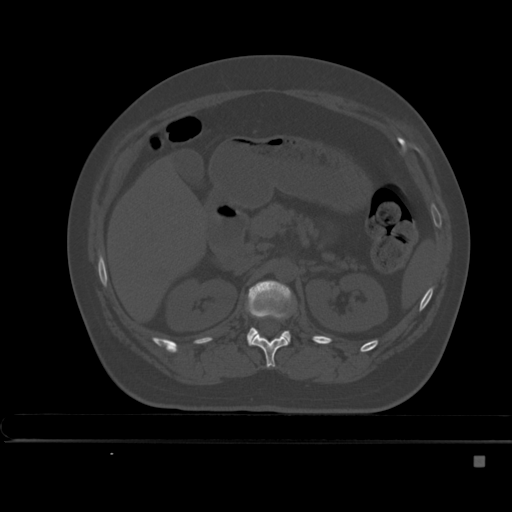
CT including the spine, one axial slice; position 205 of 495 along the scan axis; bone window (W 1800 / L 400 HU); 1.5 mm slice thickness; 512 × 512 image matrix, field of view 404 × 404 mm. Patient: female, 33 years. From the clinical record (not read from this slice): primary cancer: breast; vertebrae with lytic lesions (as recorded): T1.
Annotated regions visible in this slice (semi-automatically segmented with operator editing):
- L1 vertebra: bounding box (x1, y1, x2, y2) in pixels: (246, 280, 294, 345)
- T12 vertebra: (250, 333, 288, 368)